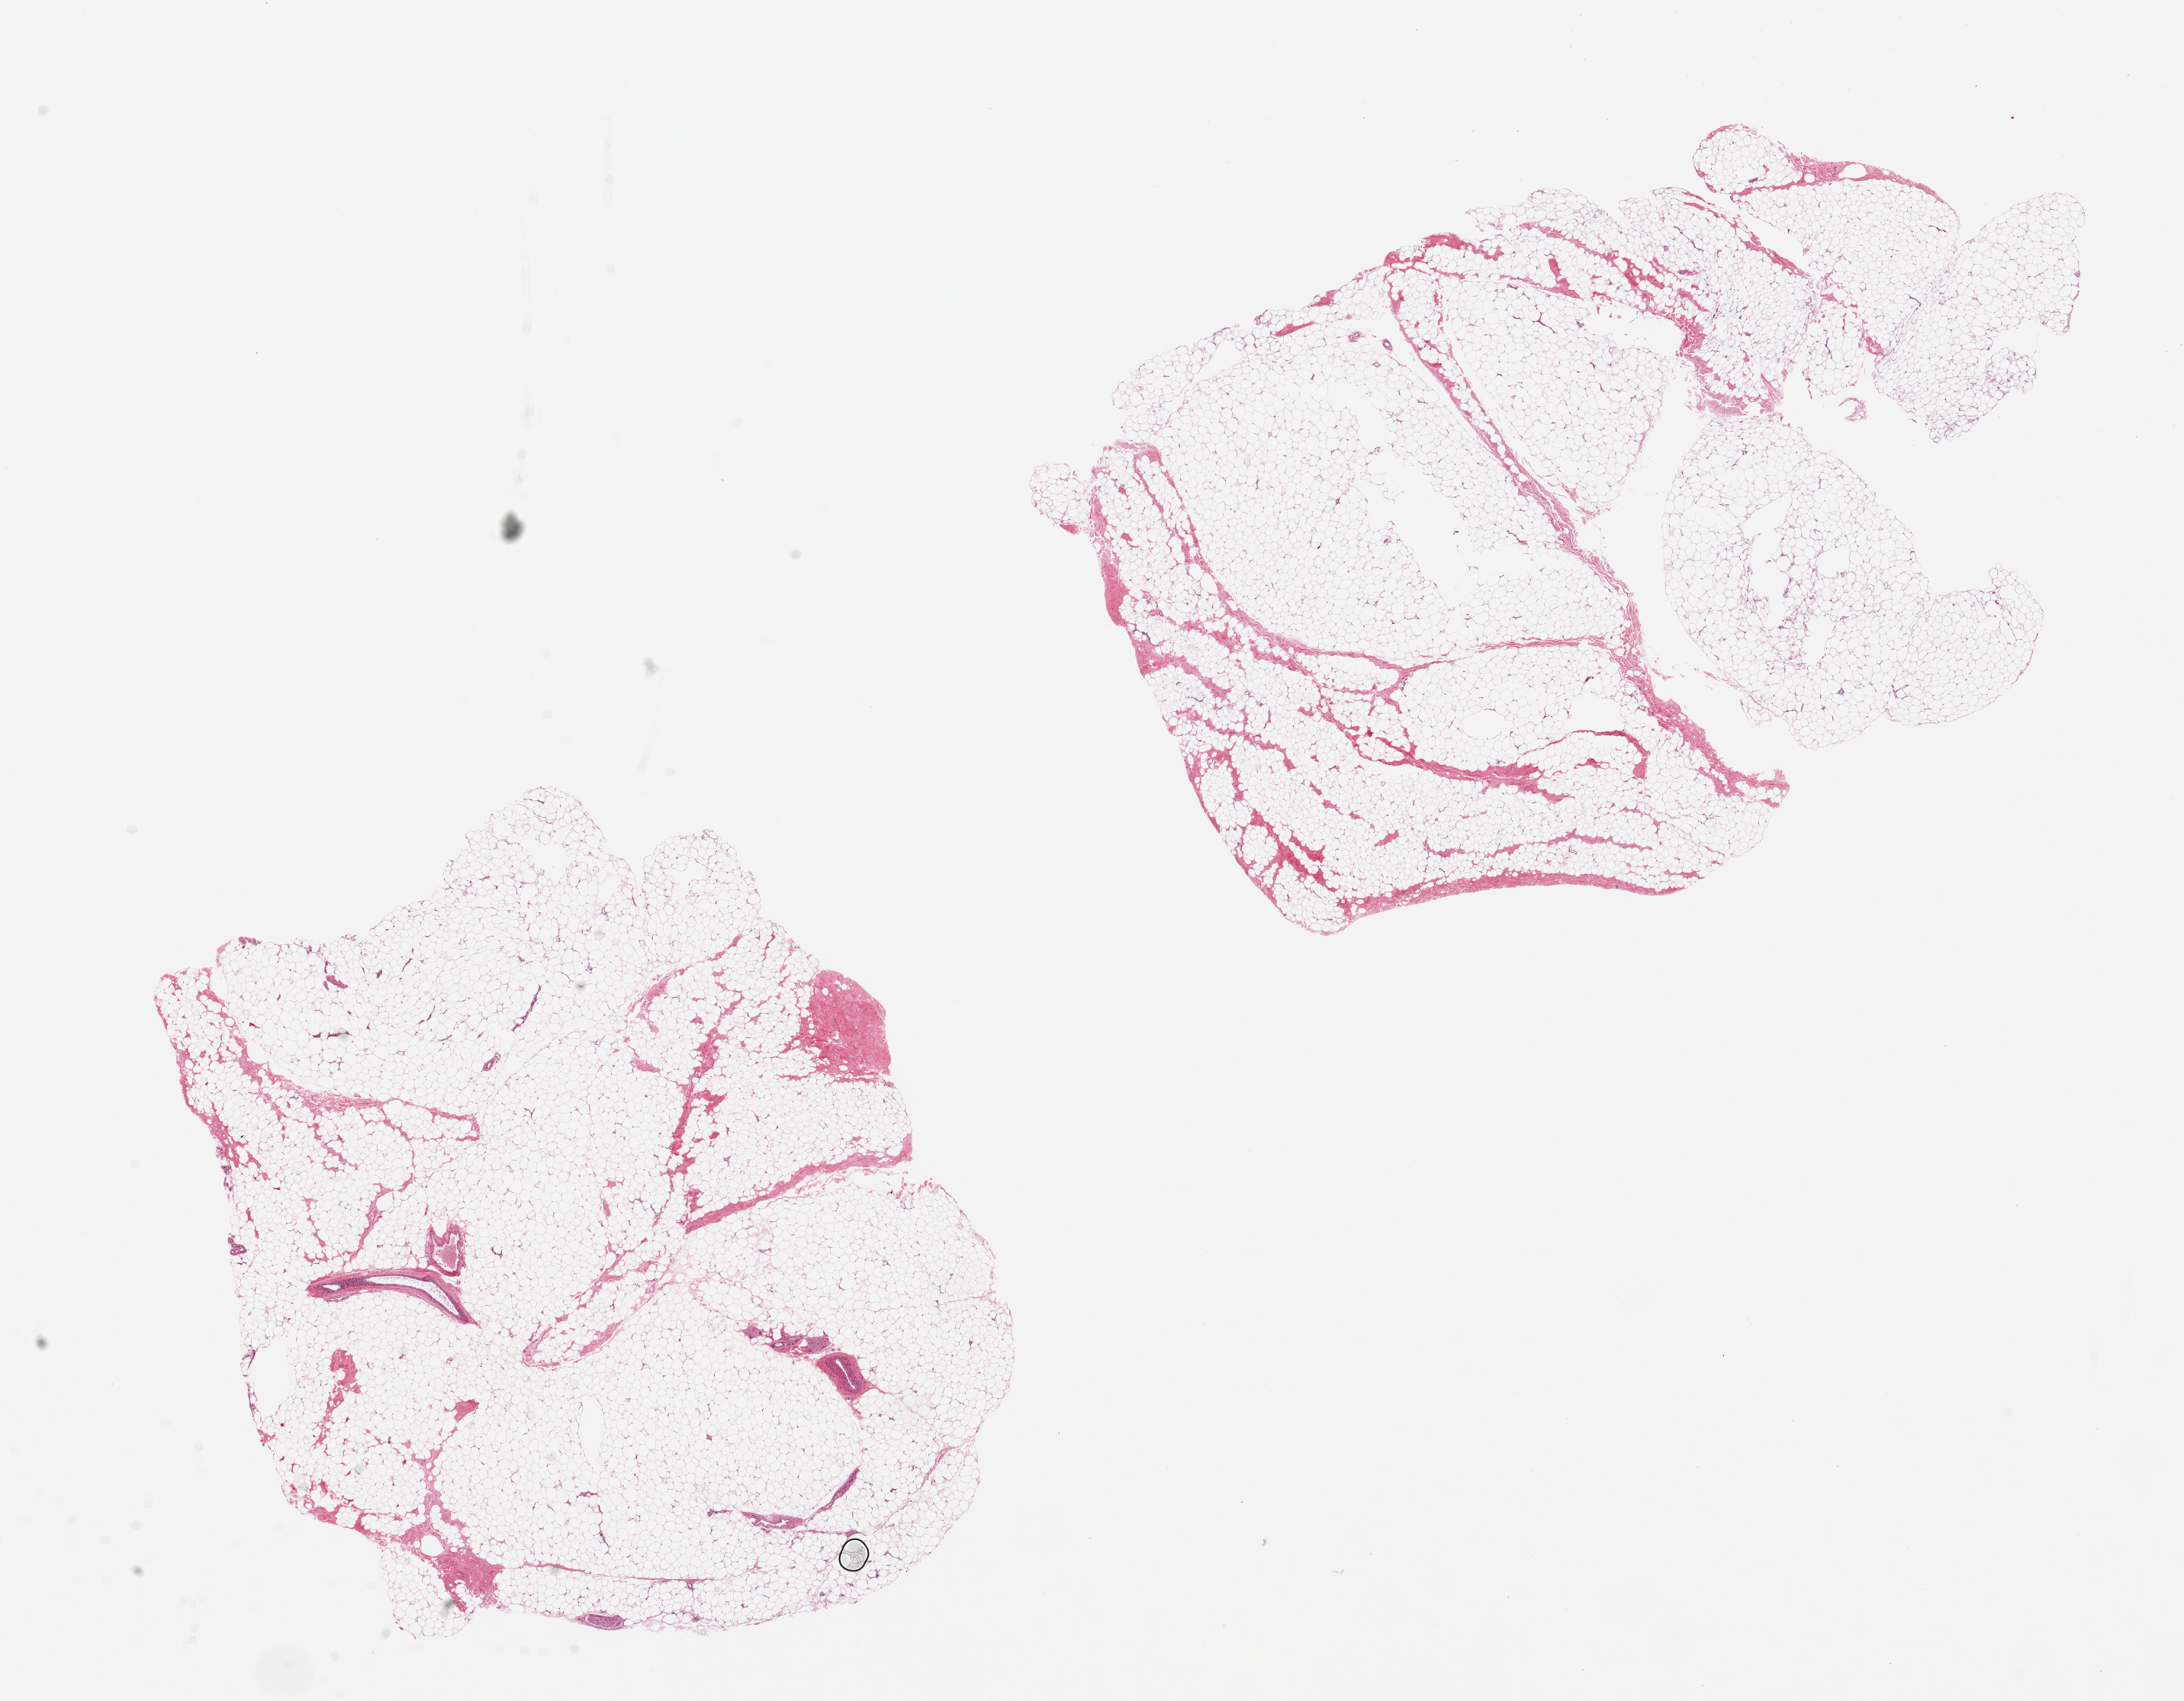
Hematoxylin and eosin (H&E) whole-slide image — whole scanned area (about 22.6 x 17.6 mm) shown as a low-resolution overview; PAXgene-fixed, paraffin-embedded tissue; target tissue: breast; tissue donor sample. Donor: male.
Reviewer comment on this tissue sample: 2 pieces, all fat, a few vessels, no ductal elements noted.